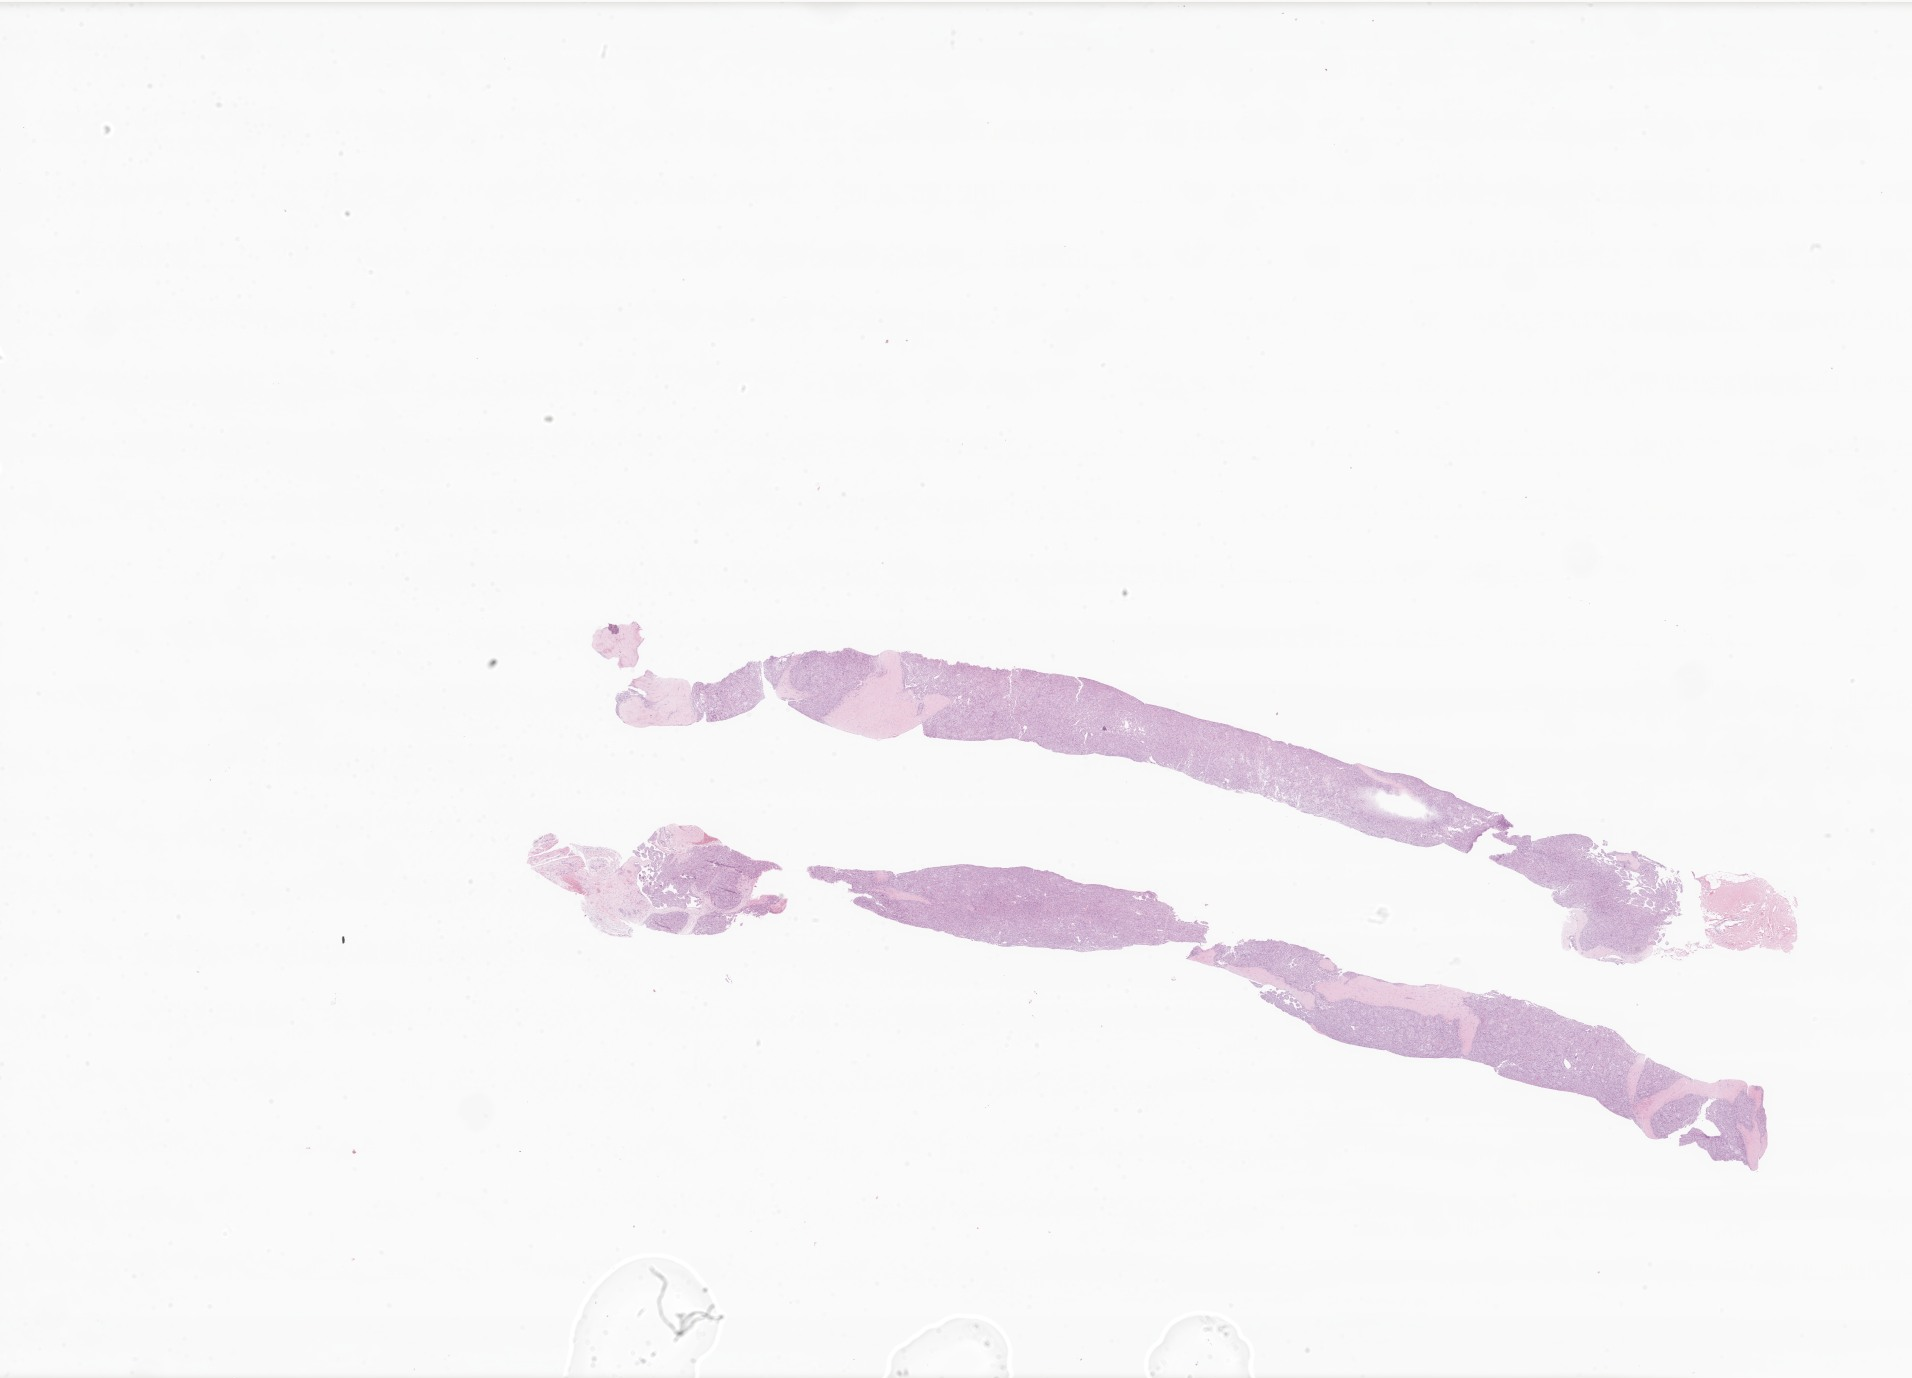
H&E whole-slide image of tumor tissue from the lower limb — whole scanned area (about 32.2 x 23.2 mm) shown as a low-resolution overview; formalin-fixed, paraffin-embedded (FFPE) tissue. Patient female; age 201 months.
* diagnosis (ICD-O-3 morphology term): Alveolar soft part sarcoma